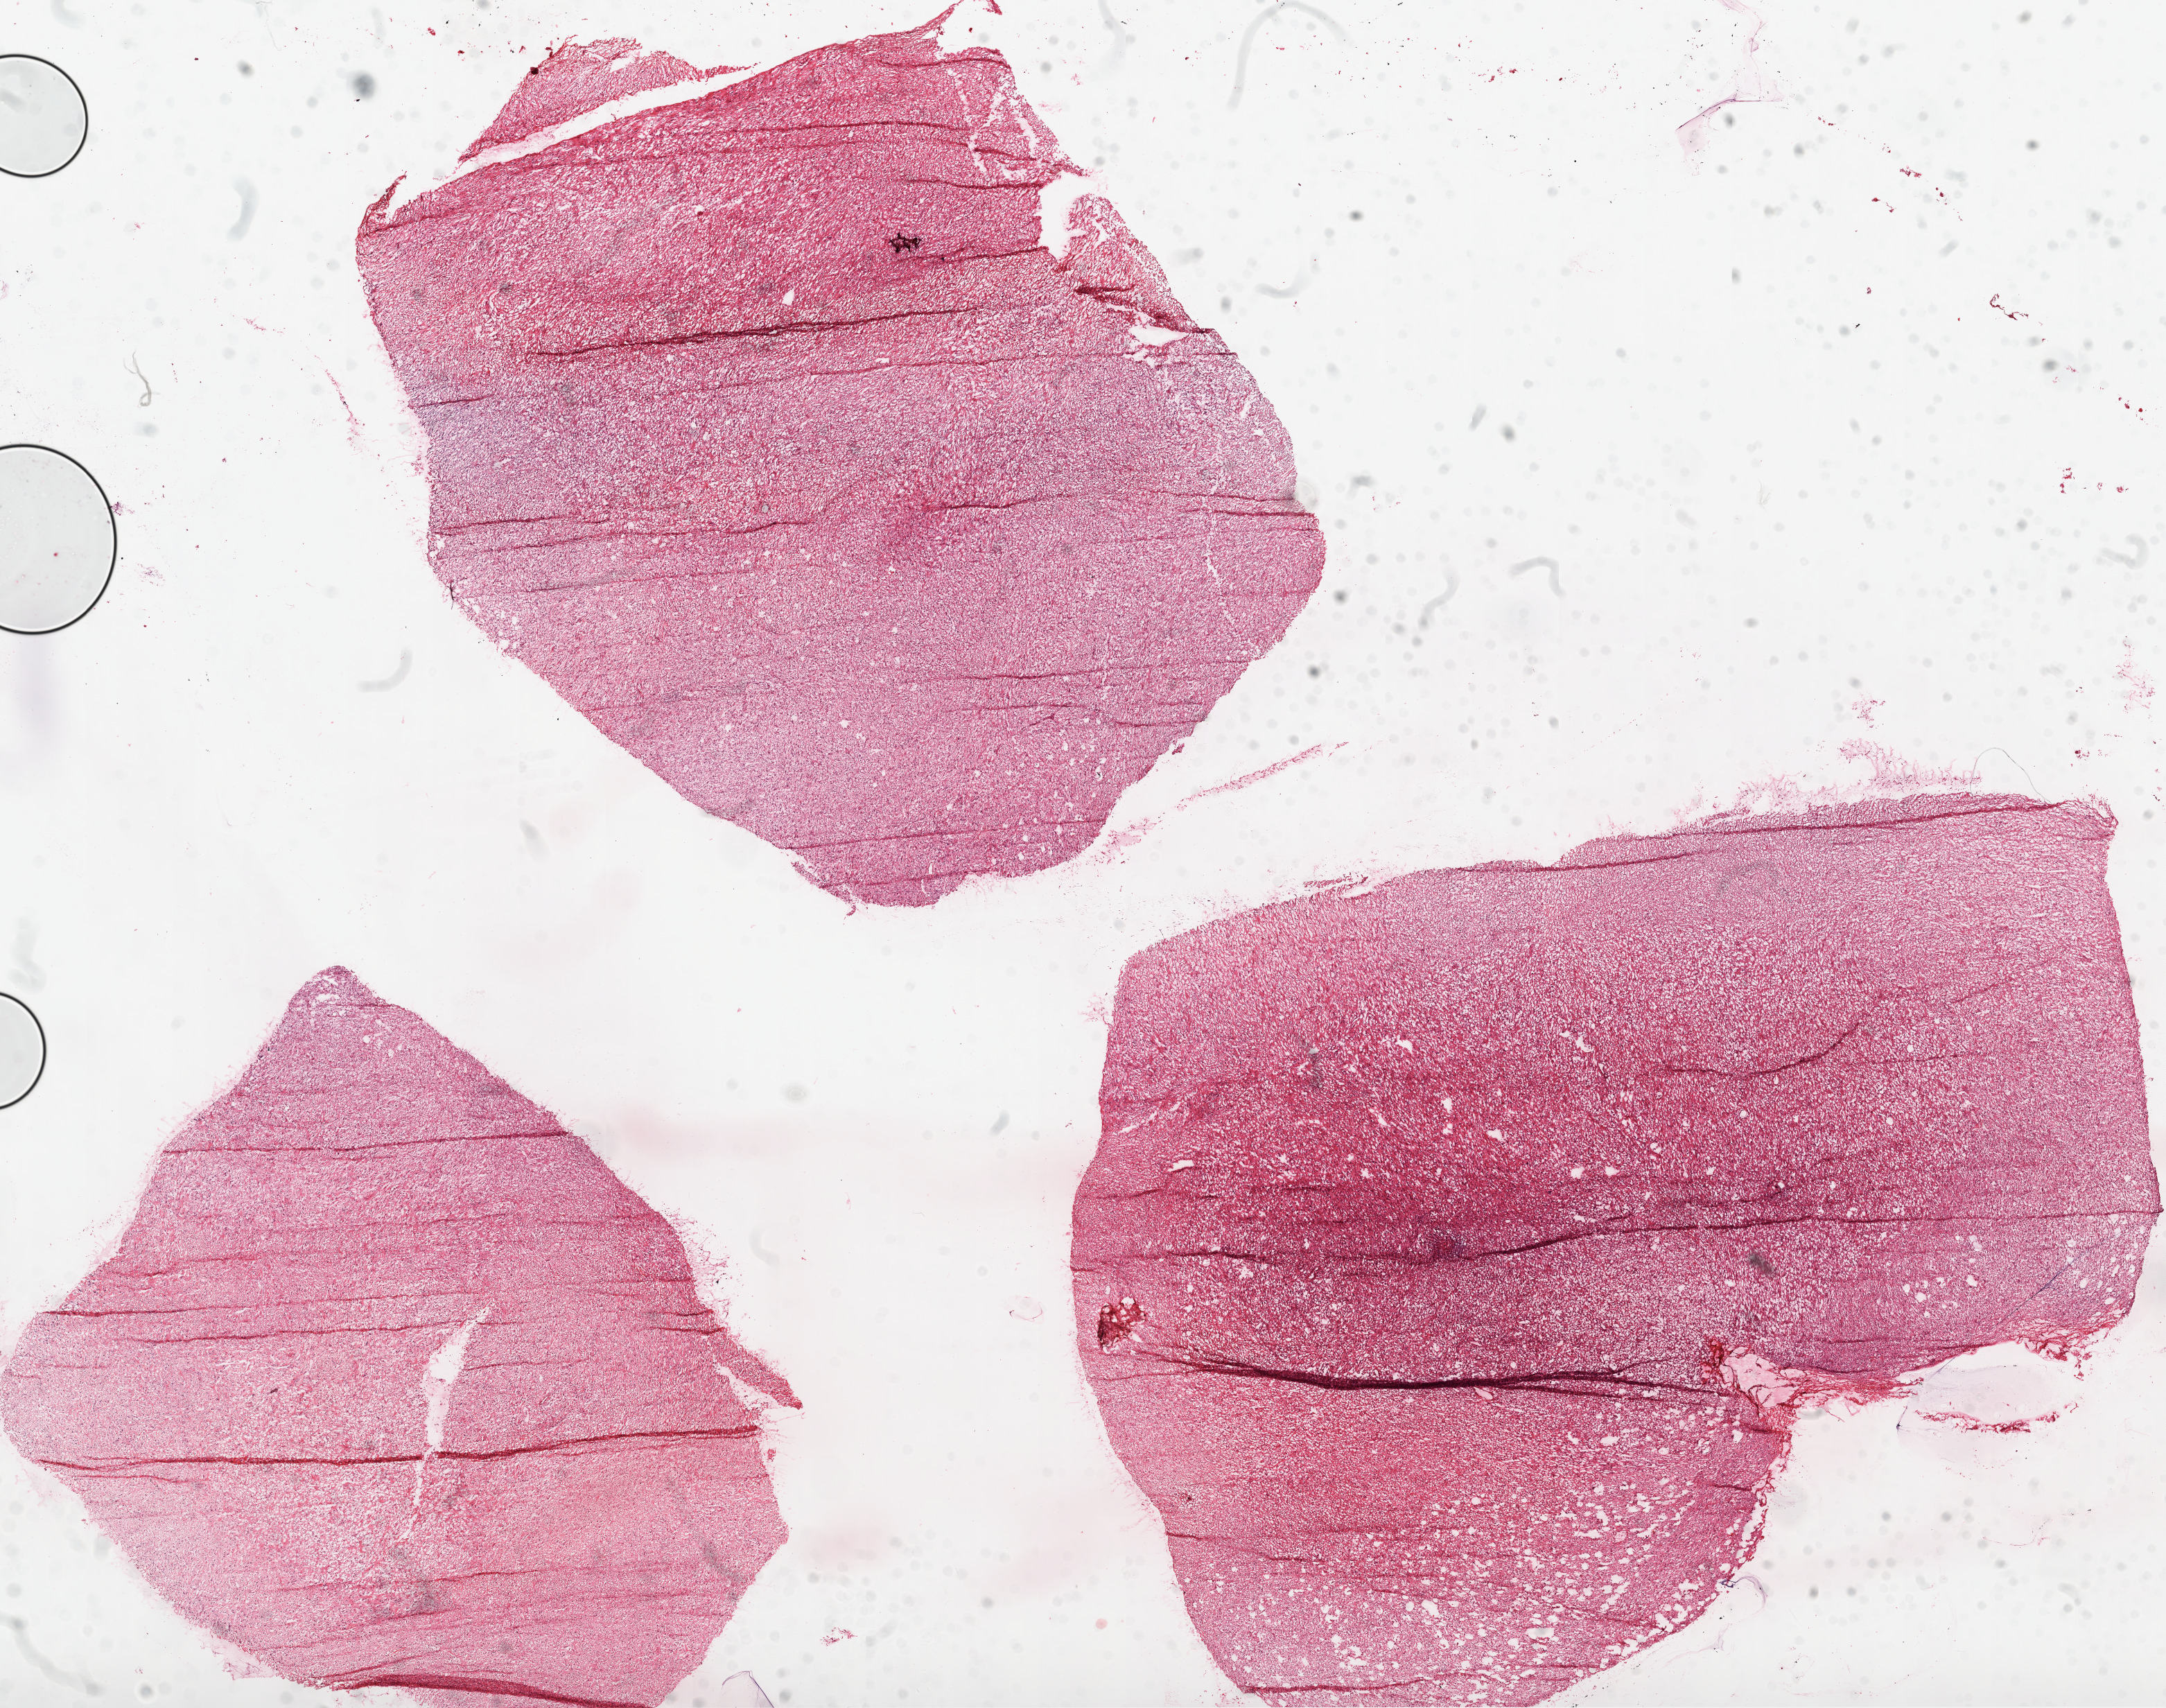
Hematoxylin and eosin (H&E) stained whole-slide image, whole scanned area (about 25.1 x 19.8 mm, acquisition: 20x scan) shown as a low-resolution overview. Frozen section. Primary tumour sample from the kidney. Male patient; age at initial diagnosis 58 years. Histologic grade: G3 (poorly differentiated). Slide review estimates, as recorded: tumour cells 95%, tumour nuclei 90%, normal cells 0%, stromal cells 5%, necrosis 0%.
Pathologic diagnosis: Clear cell adenocarcinoma, NOS. AJCC pathologic stage: III.